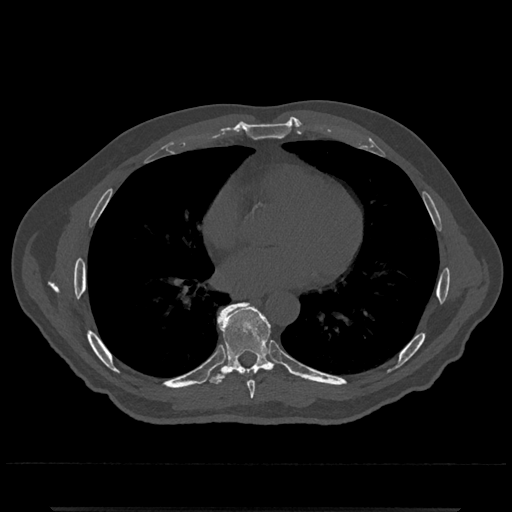
CT including the spine, one axial slice. Slice 687 of 797 in the series (ordered by position). Reconstruction kernel Br40s/3. Bone window (W 1800 / L 400 HU). 512 × 512 image matrix, field of view 393 × 393 mm. Patient: male, 67 years. Case-level facts recorded for this patient, not image findings: primary cancer: prostate.
Structures marked on this image (semi-automatic segmentation, software-assisted and operator-edited):
- T7 vertebra: box from (x=247, y=381) to (x=255, y=399) px
- T8 vertebra: (x=206, y=302)–(x=286, y=386)